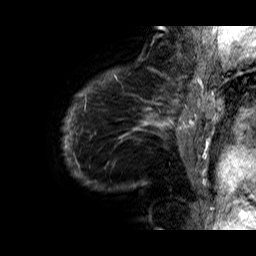
Breast MRI (dynamic contrast-enhanced), one sagittal slice; slice 1 of 60 in the series (ordered by position); dynamic contrast-enhanced series, time point 2 of 6 at this slice position (early post-contrast); 1.5 T; TE 6.3 ms, TR 32.9 ms; 4 mm slice thickness; 256 × 256 image matrix. Female patient. Case-level facts recorded for this patient, not image findings: setting: breast cancer imaged before/during neoadjuvant chemotherapy; receptor status: HR-positive, HER2-negative.
Annotated regions visible in this slice (semi-automatic segmentation, software-assisted and operator-edited):
- analysis volume of interest (the breast-tissue region the enhancement analysis was run in; not a lesion): bounding box <62,74,176,200> (left, top, right, bottom; pixels)
- tumour enhancement mask (voxels above the 100 % enhancement threshold inside the analysis volume of interest): <62,74,176,185>